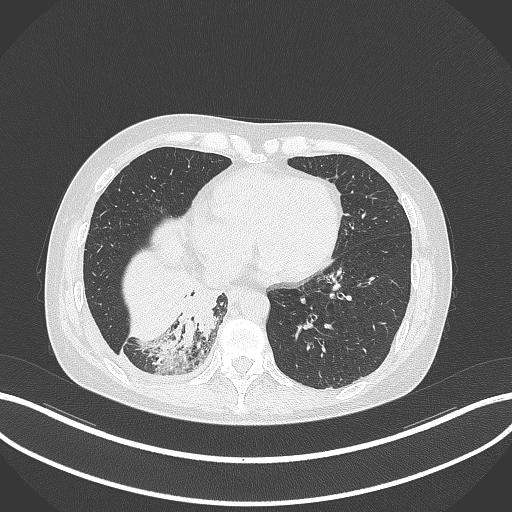
Chest CT, one axial slice; slice 95 of 329 in the series (ordered by position); lung window (W 1500 / L -600 HU); 1 mm slice thickness; 512 × 512 image matrix, field of view 400 × 400 mm. Patient: female, 63 years. From the clinical record (not read from this slice): clinical TNM (as recorded): T1c N0 M0.
Annotated regions visible in this slice (bounding box drawn by a radiologist):
- lung tumour (recorded histology: adenocarcinoma): bounding box <163,278,226,350> (left, top, right, bottom; pixels)